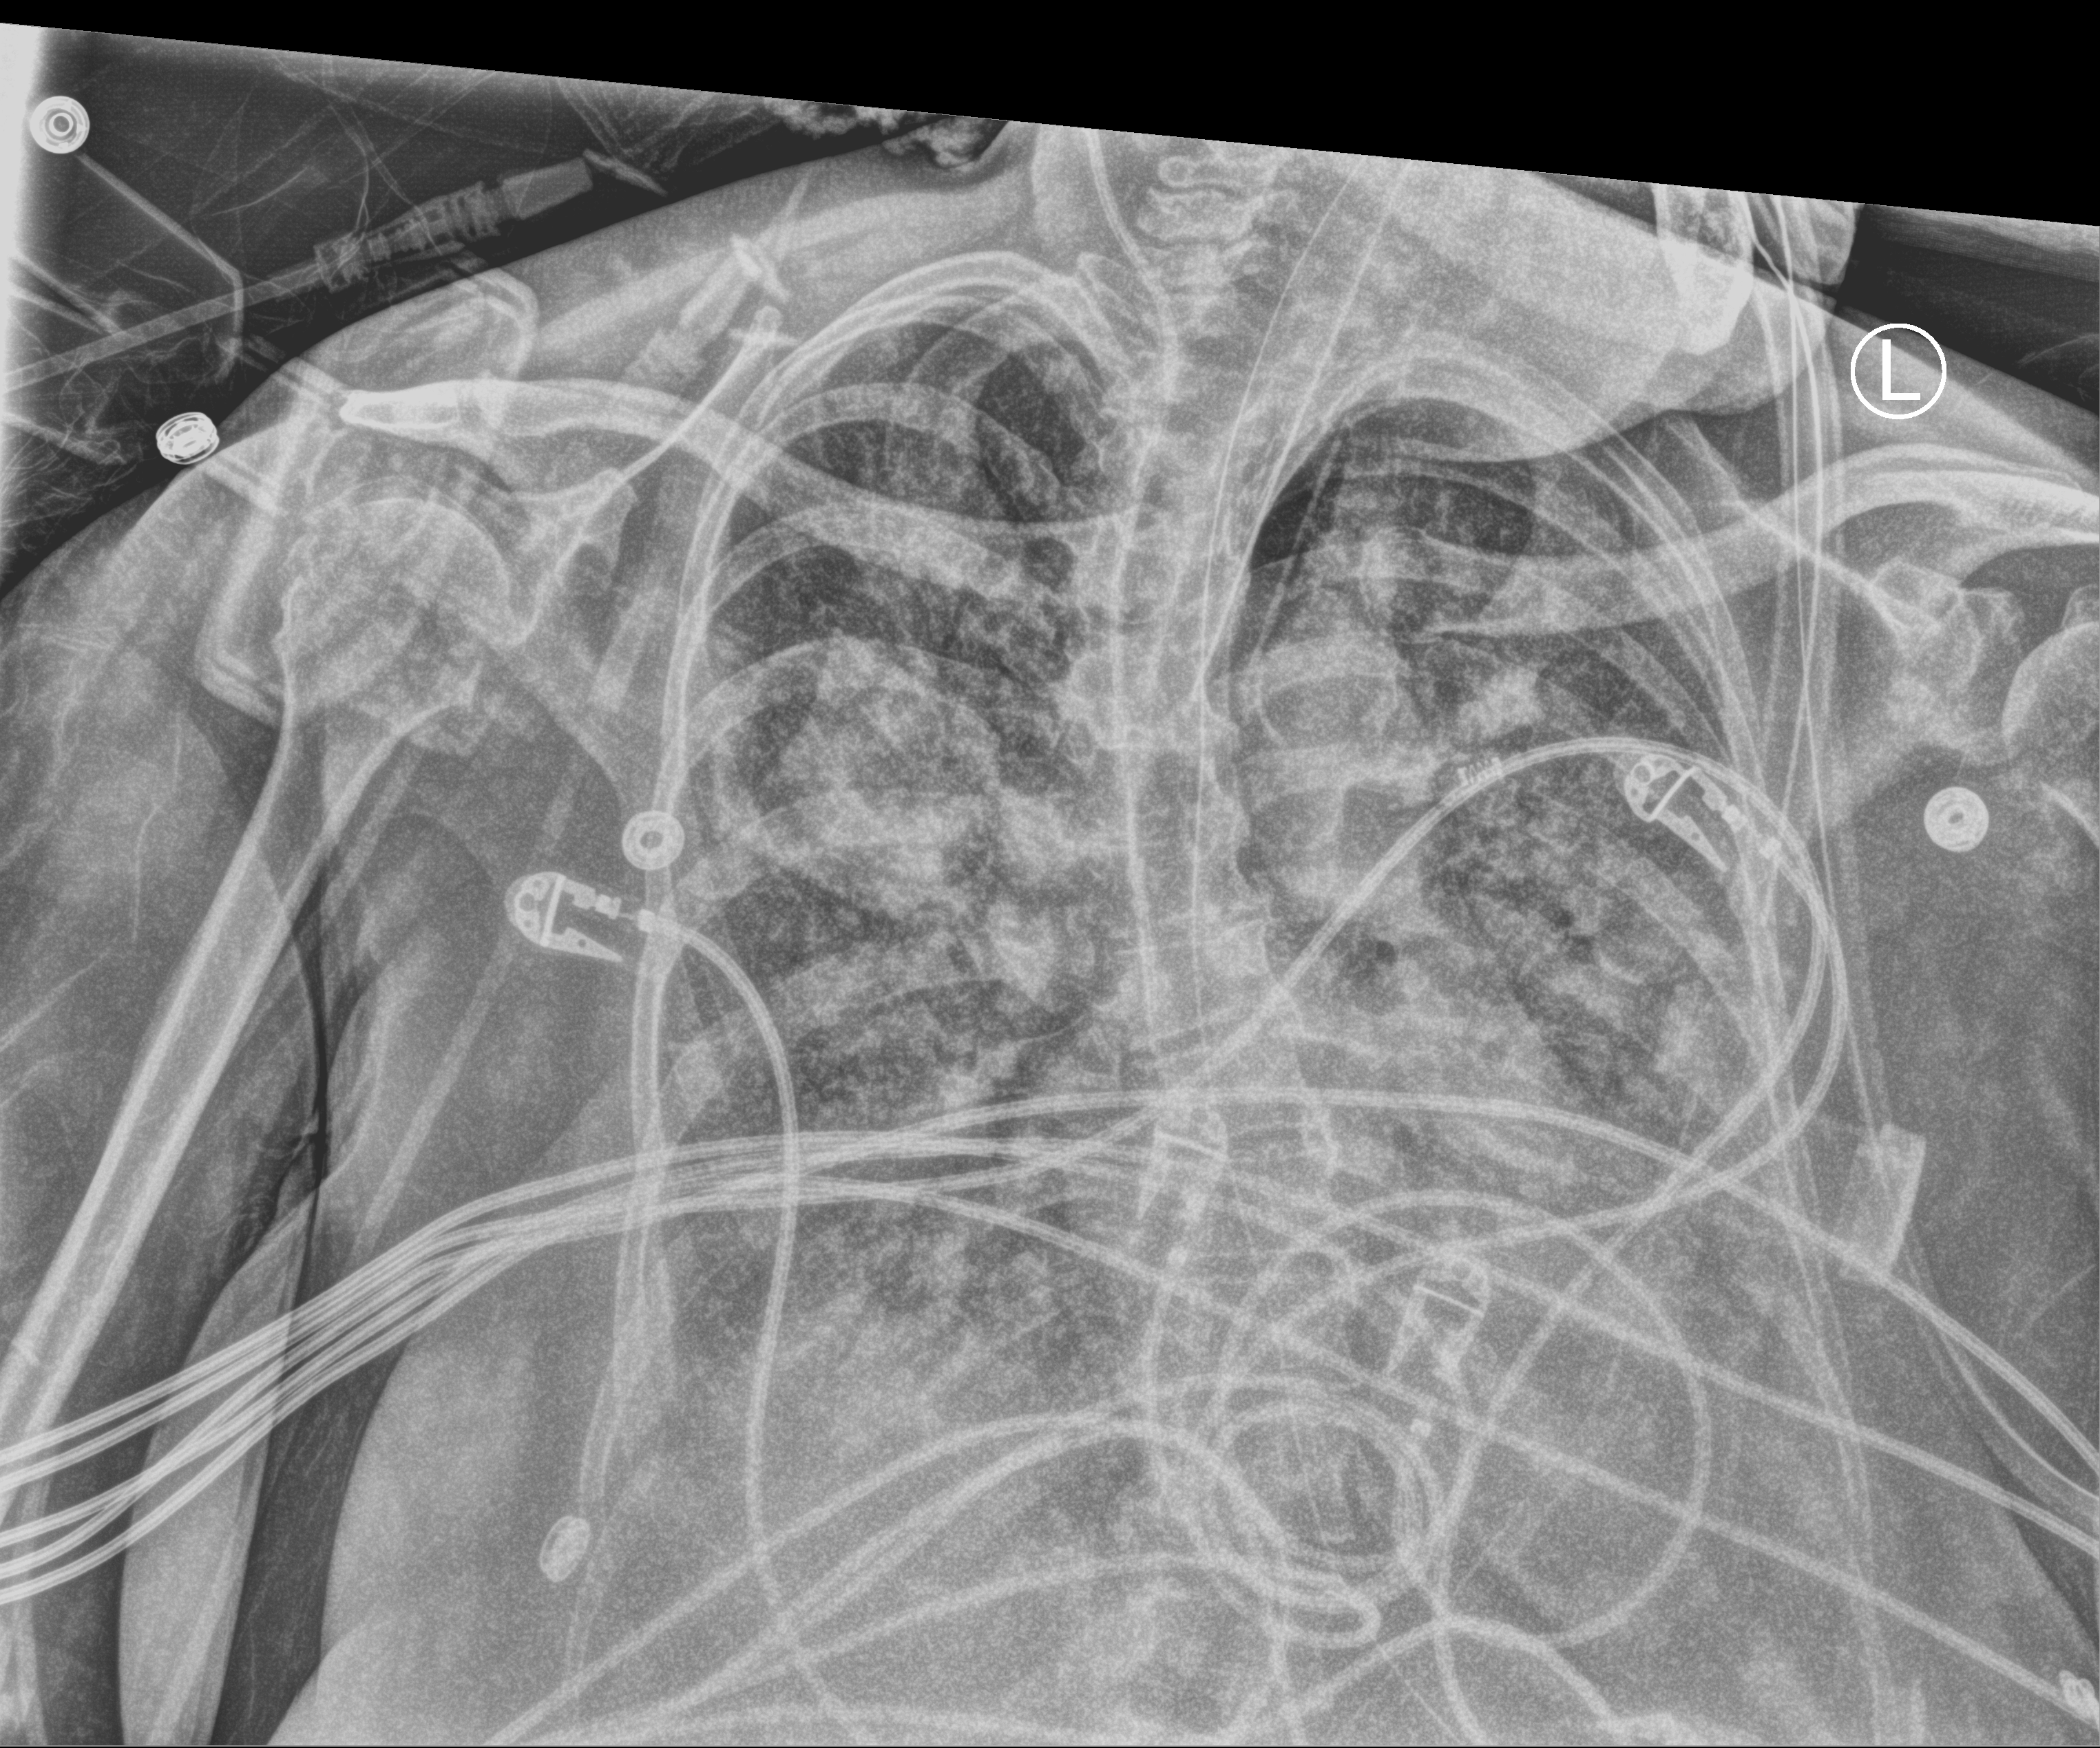
Bedside chest radiograph (computed radiography); anteroposterior (AP) projection. Patient hospitalised with COVID-19; female, aged 60–74 years.
From the hospital-stay record, not from the radiograph (when in the stay this image was taken is not recorded):
- admitted to intensive care during this hospital stay: yes
- diabetes (admission record): no